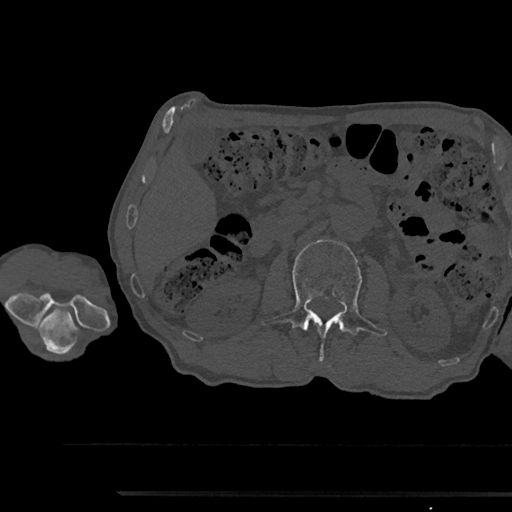
CT including the spine, one axial slice; reconstruction kernel Br40s/3; bone window (W 1800 / L 400 HU); 512 × 512 image matrix, field of view 367 × 367 mm. Male patient, age 79 years. From the clinical record (not read from this slice): primary cancer: prostate.
Outlined on this slice (semi-automatically segmented with operator editing):
- L2 vertebra: bounding box (x1, y1, x2, y2) in pixels: (260, 240, 387, 364)